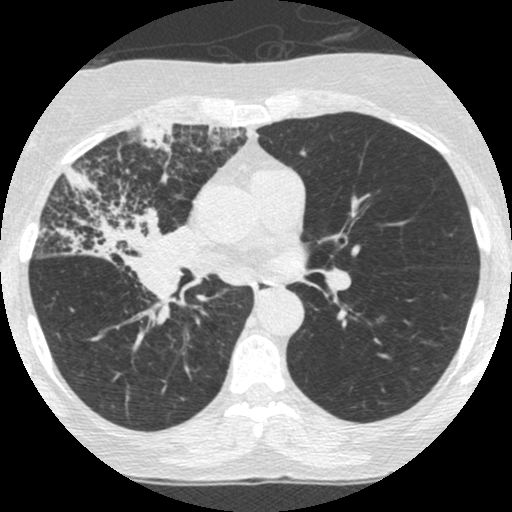
Low-dose screening chest CT, one axial slice. Position 143 of 253 along the scan axis. 120 kVp. Lung window (W 1500 / L -600 HU). 512 × 512 image matrix, field of view 294 × 294 mm.
Annotated regions visible in this slice (manually delineated by an expert):
- lesion 2 (tumor, hilum of right lung): bounding box (x1, y1, x2, y2) in pixels: (38, 166, 187, 328)
- lesion 3 (tumor, upper lobe of right lung): (136, 124, 175, 182)
- lesion 4 (tumor, upper lobe of right lung): (206, 125, 242, 150)